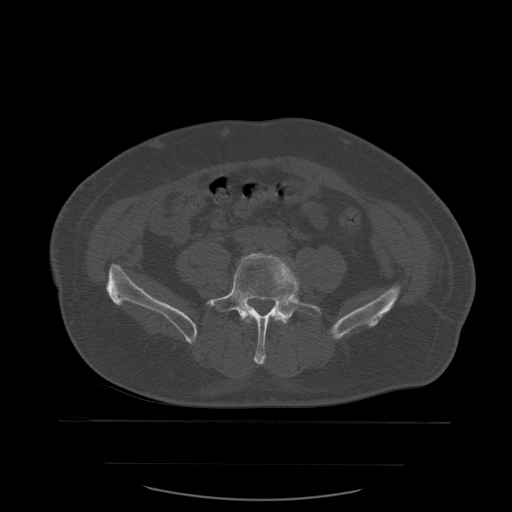
CT including the spine, one axial slice; slice 143 of 590 in the series (ordered by position); bone window (W 1800 / L 400 HU); 1.25 mm slice thickness; 512 × 512 image matrix. Patient age 71 years. From the clinical record (not read from this slice): primary cancer: lung.
Outlined on this slice (semi-automatic segmentation, software-assisted and operator-edited):
- L4 vertebra: bounding box (x1, y1, x2, y2) in pixels: (244, 315, 280, 324)
- L5 vertebra: (206, 253, 322, 365)